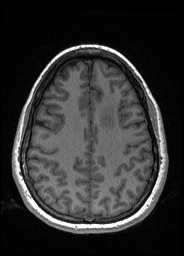
Pre-operative brain MRI before brain-tumour surgery, one axial slice; slice 66 of 176 in the series (ordered by position); T1-weighted post-contrast; 1 mm slice thickness; 184 × 256 image matrix. Case-level facts recorded for this patient, not image findings: histopathology: Oligodendroglioma; WHO grade: 2; IDH mutation: yes.
Annotated regions visible in this slice (manually delineated by an expert):
- tumour: box from (x=100, y=104) to (x=116, y=127) px